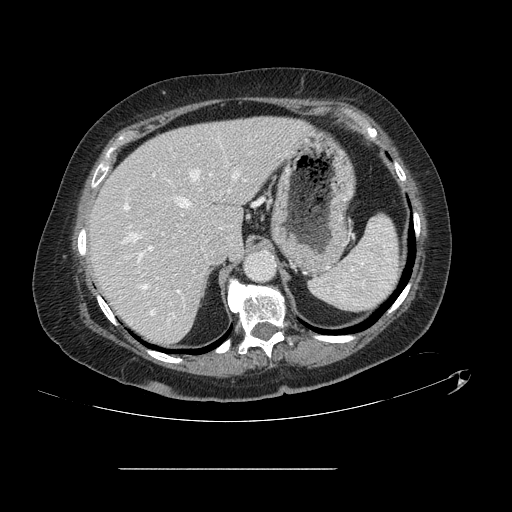
Contrast-enhanced abdominal CT, one axial slice; slice 97 of 148 in the series (ordered by position); 120 kVp; soft-tissue window (W 400 / L 40 HU); 2.5 mm slice thickness; 512 × 512 image matrix. Female patient, age 75 years. From the clinical record (not read from this slice): diagnosis: colorectal cancer liver metastases, imaged before liver resection; multiple liver metastases: no; largest metastasis: 2.4 cm.
Outlined on this slice (manually delineated by an expert):
- hepatic veins: bounding box <133,170,247,315> (left, top, right, bottom; pixels)
- liver: <90,117,306,345>
- planned liver remnant (the part of the liver to remain after resection): <90,117,307,345>
- portal vein (with intrahepatic branches): <125,173,211,293>